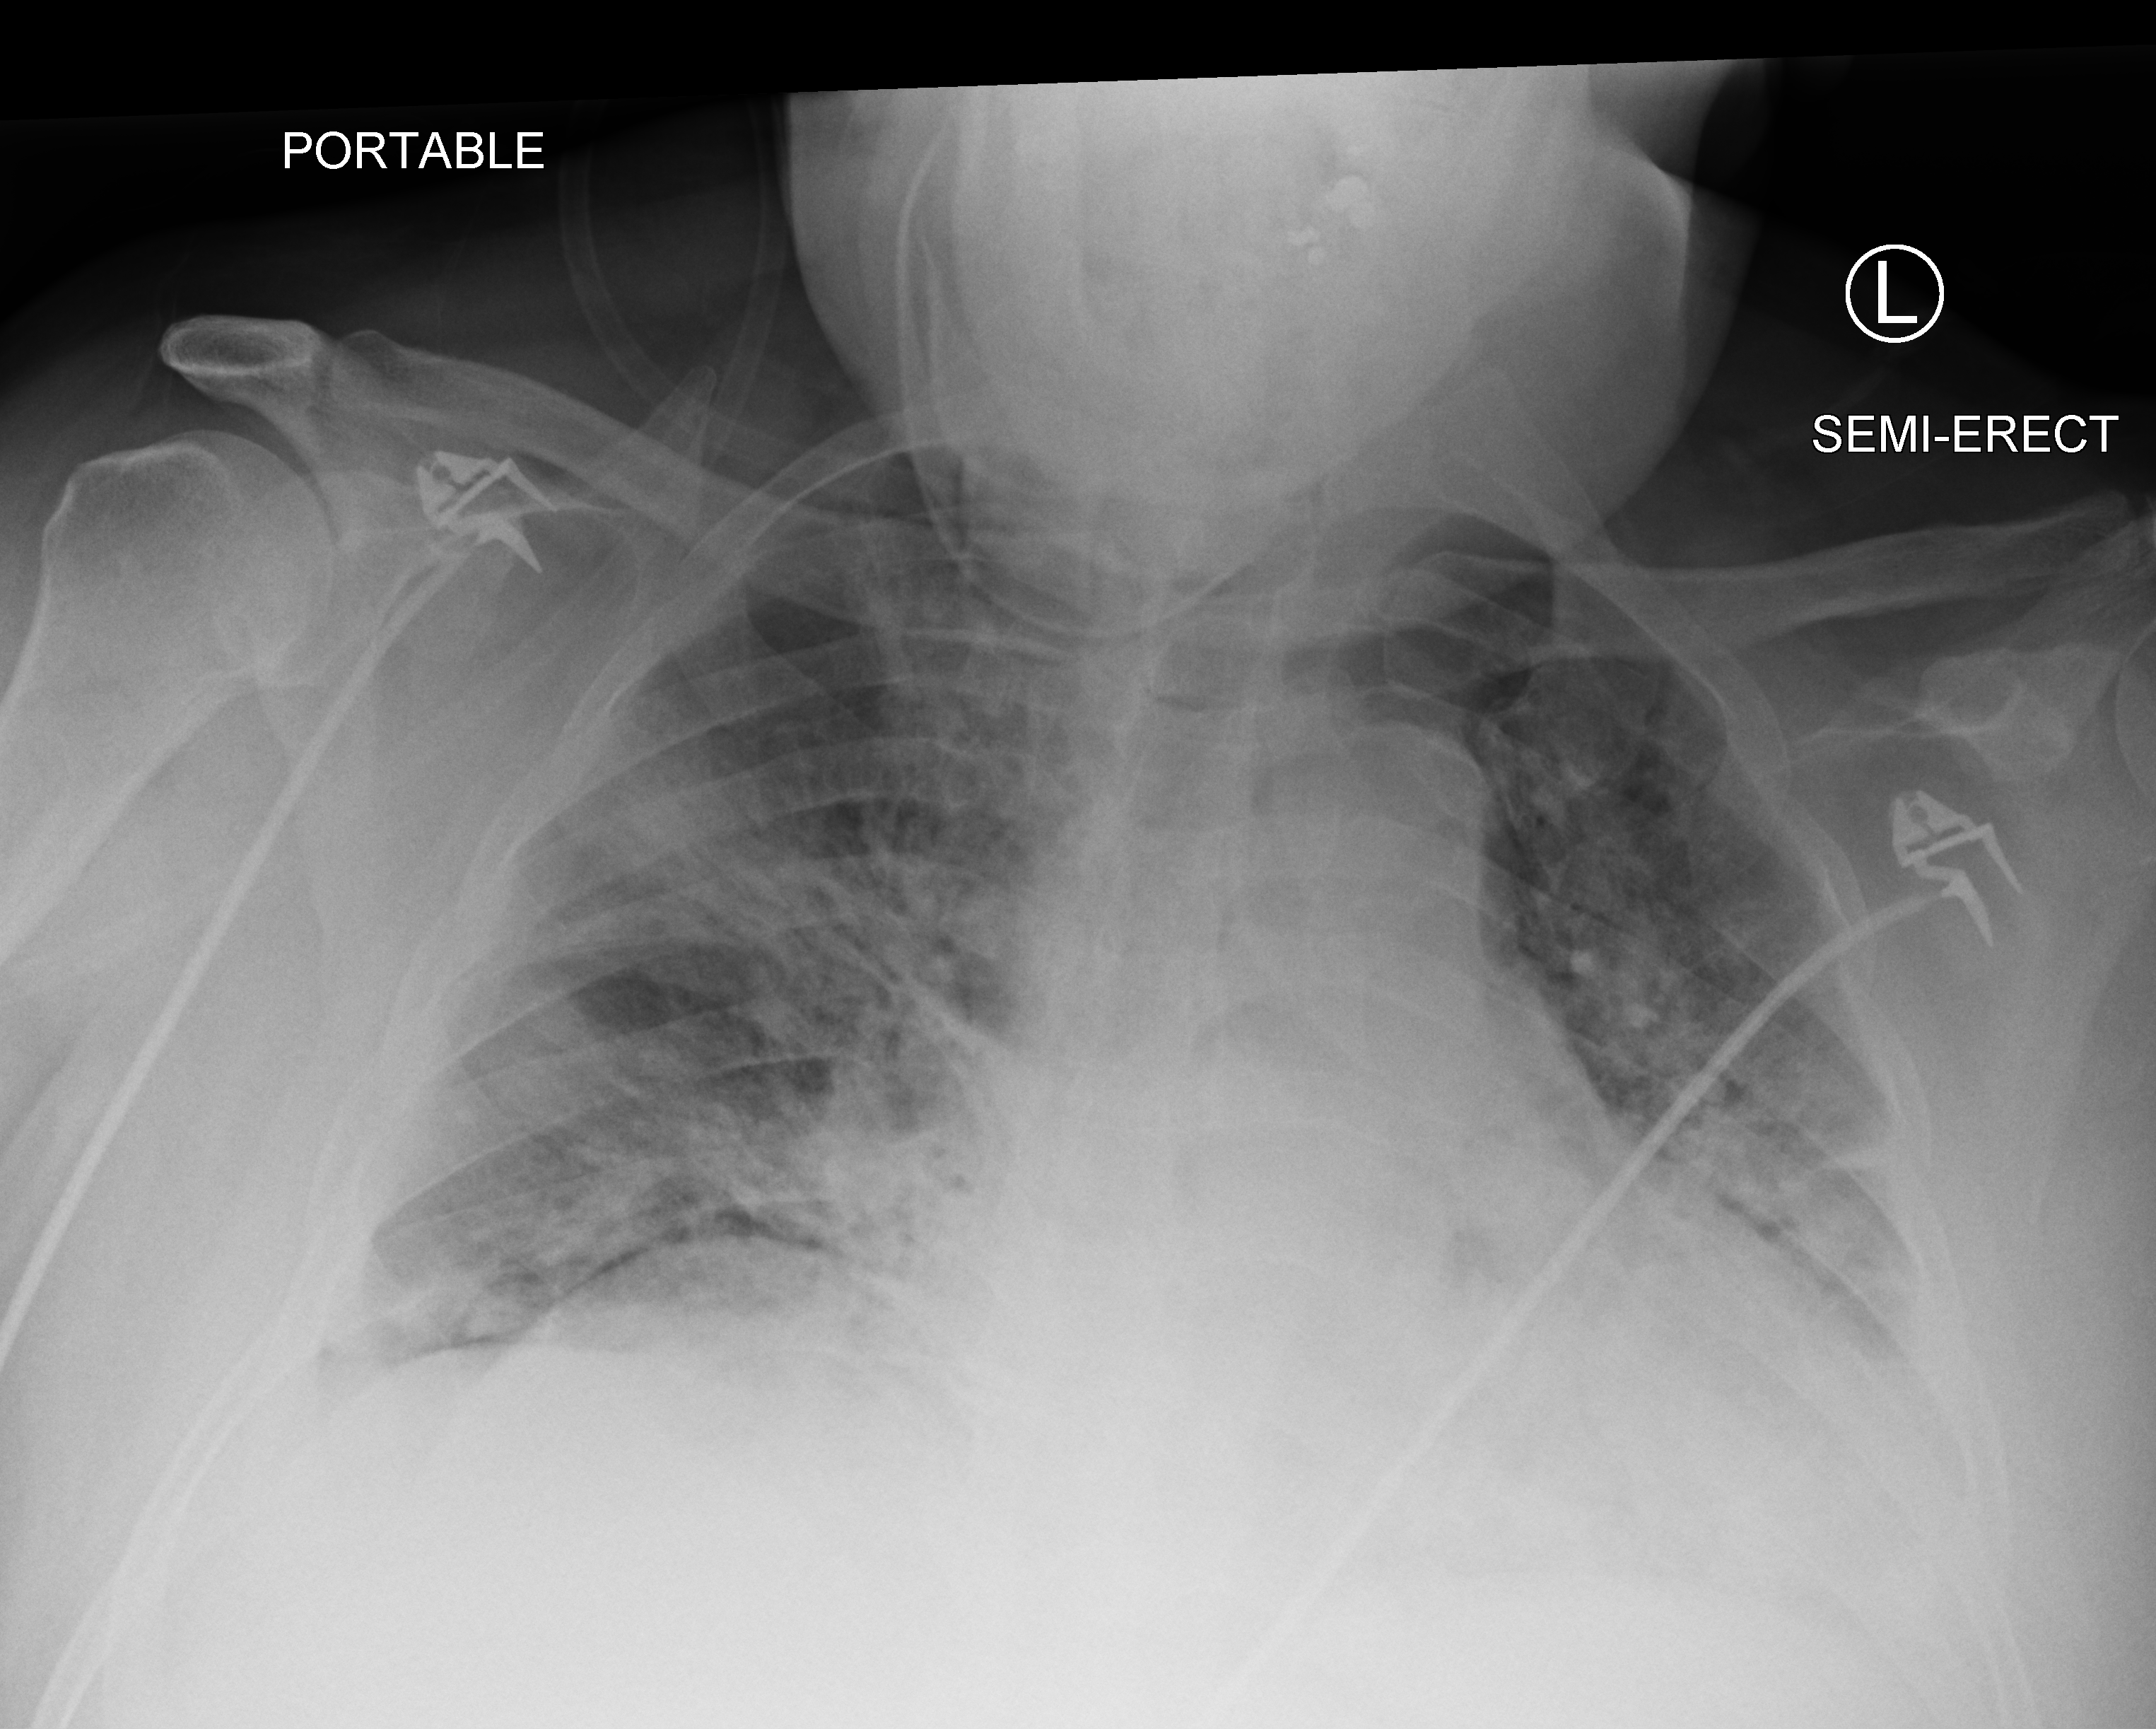
Portable chest radiograph, anteroposterior (AP) projection. Male patient hospitalised with COVID-19, age 60–74 years.
Admission-level facts for this patient (not findings on this image; timing relative to this image not recorded): other chronic lung disease (admission record): no; admitted to intensive care during this hospital stay: yes.